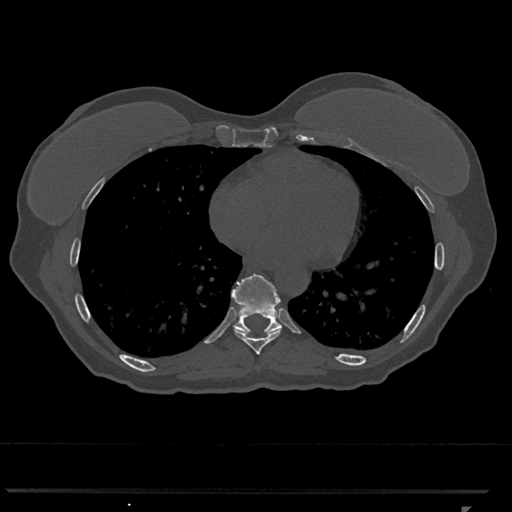
CT including the spine, one axial slice. Slice 646 of 793 in the series (ordered by position). 120 kVp. Bone window (W 1800 / L 400 HU). 0.5 mm slice thickness. 512 × 512 image matrix, field of view 380 × 380 mm. Patient: female, 62 years. Case-level facts recorded for this patient, not image findings: primary cancer: renal.
Annotated regions visible in this slice (semi-automatically segmented with operator editing):
- T8 vertebra: bounding box (x1, y1, x2, y2) in pixels: (235, 330, 281, 355)
- T9 vertebra: (232, 274, 282, 335)